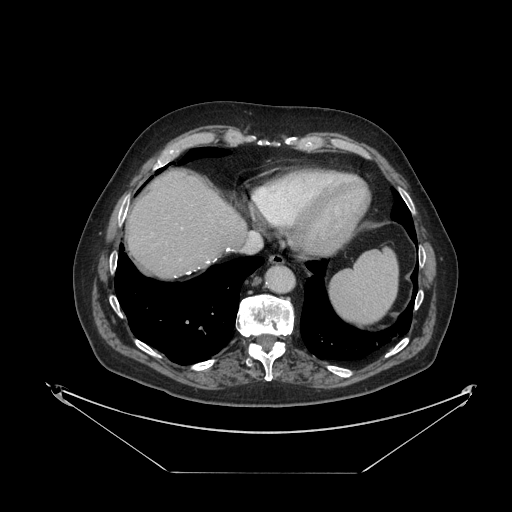
Contrast-enhanced abdominal CT, one axial slice; slice 106 of 121 in the series (ordered by position); 120 kVp; intravenous contrast given; soft-tissue window (W 400 / L 40 HU); 2.5 mm slice thickness; 512 × 512 image matrix, field of view 500 × 500 mm. Male patient, age 68 years. From the clinical record (not read from this slice): diagnosis: colorectal cancer liver metastases, imaged before liver resection; multiple liver metastases: no; largest metastasis: 4 cm; disease in both lobes: no.
Outlined on this slice (outlined manually by an expert reader):
- liver: bounding box [x1, y1, x2, y2] px = [128, 172, 246, 277]
- planned liver remnant (the part of the liver to remain after resection): [128, 172, 246, 277]